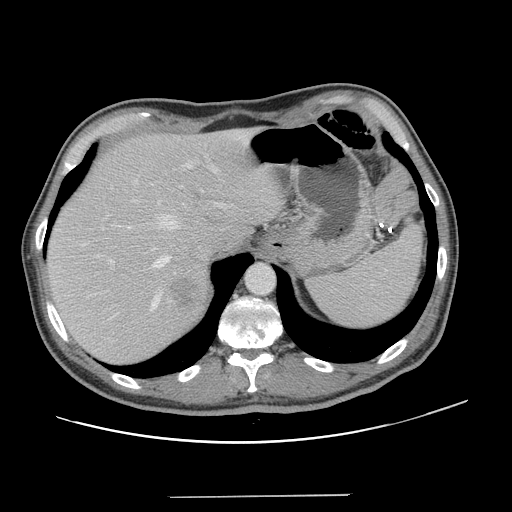
Contrast-enhanced abdominal CT, one axial slice; position 101 of 131 along the scan axis; 120 kVp; soft-tissue window (W 400 / L 40 HU); 2.5 mm slice thickness; 512 × 512 image matrix, field of view 403 × 403 mm. Male patient, age 60 years. From the clinical record (not read from this slice): diagnosis: colorectal cancer liver metastases, imaged before liver resection; multiple liver metastases: no; largest metastasis: 2.5 cm; disease in both lobes: no.
Outlined on this slice (manually delineated by an expert):
- hepatic veins: box from (x=82, y=166) to (x=217, y=311) px
- liver: (x=47, y=129)–(x=281, y=364)
- planned liver remnant (the part of the liver to remain after resection): (x=47, y=129)–(x=281, y=351)
- portal vein (with intrahepatic branches): (x=94, y=156)–(x=233, y=265)
- liver metastasis: (x=172, y=279)–(x=199, y=311)